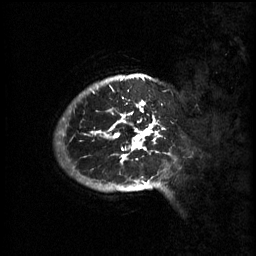
Breast MRI (dynamic contrast-enhanced), one sagittal slice. Position 52 of 60 along the scan axis. 3 images stored at this slice position (order not interpretable as contrast timing). 1.5 T. TE 4.2 ms, TR 11 ms. 2 mm slice thickness. 256 × 256 image matrix, field of view 220 × 220 mm. Patient: female, 51 years.
Outlined on this slice (semi-automatic segmentation, software-assisted and operator-edited):
- analysis volume of interest (the breast-tissue region the enhancement analysis was run in; not a lesion): bounding box (x1, y1, x2, y2) in pixels: (63, 80, 177, 193)
- tumour enhancement mask (voxels above the 70 % enhancement threshold inside the analysis volume of interest): (91, 80, 170, 191)